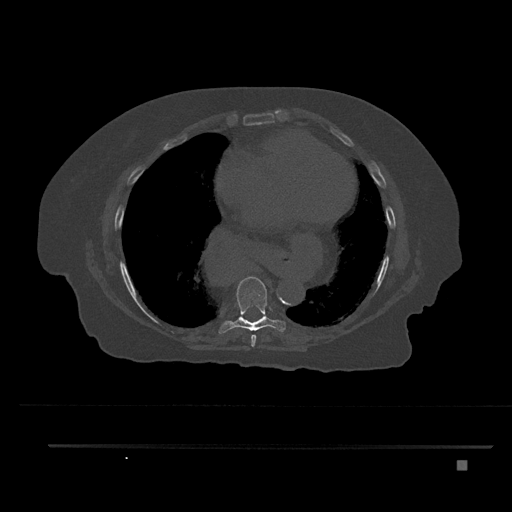
CT including the spine, one axial slice; position 446 of 797 along the scan axis; 120 kVp; bone window (W 1800 / L 400 HU); 0.5 mm slice thickness; 512 × 512 image matrix, field of view 437 × 437 mm. Patient: female, 76 years. From the clinical record (not read from this slice): primary cancer: lung; vertebrae with lytic lesions (as recorded): T11, L3.
Annotated regions visible in this slice (semi-automatic segmentation, software-assisted and operator-edited):
- T7 vertebra: bounding box (x1, y1, x2, y2) in pixels: (251, 334, 256, 347)
- T8 vertebra: (218, 276, 286, 334)